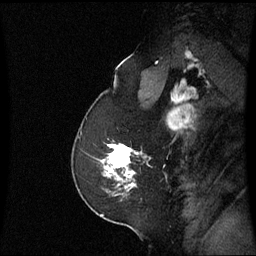
Breast MRI (dynamic contrast-enhanced), one sagittal slice. Dynamic contrast-enhanced series, image 2 of 3 at this slice position (ordered by acquisition). 1.5 T. TE 4.2 ms, TR 8.9 ms. 256 × 256 image matrix, field of view 220 × 220 mm. Patient: female, 58 years. From the clinical record (not read from this slice): setting: breast cancer imaged before/during neoadjuvant chemotherapy; receptor status: triple-negative.
Structures marked on this image (semi-automatically segmented with operator editing):
- analysis volume of interest (the breast-tissue region the enhancement analysis was run in; not a lesion): bounding box <104,140,151,193> (left, top, right, bottom; pixels)
- tumour enhancement mask (voxels above the 70 % enhancement threshold inside the analysis volume of interest): <108,144,135,187>